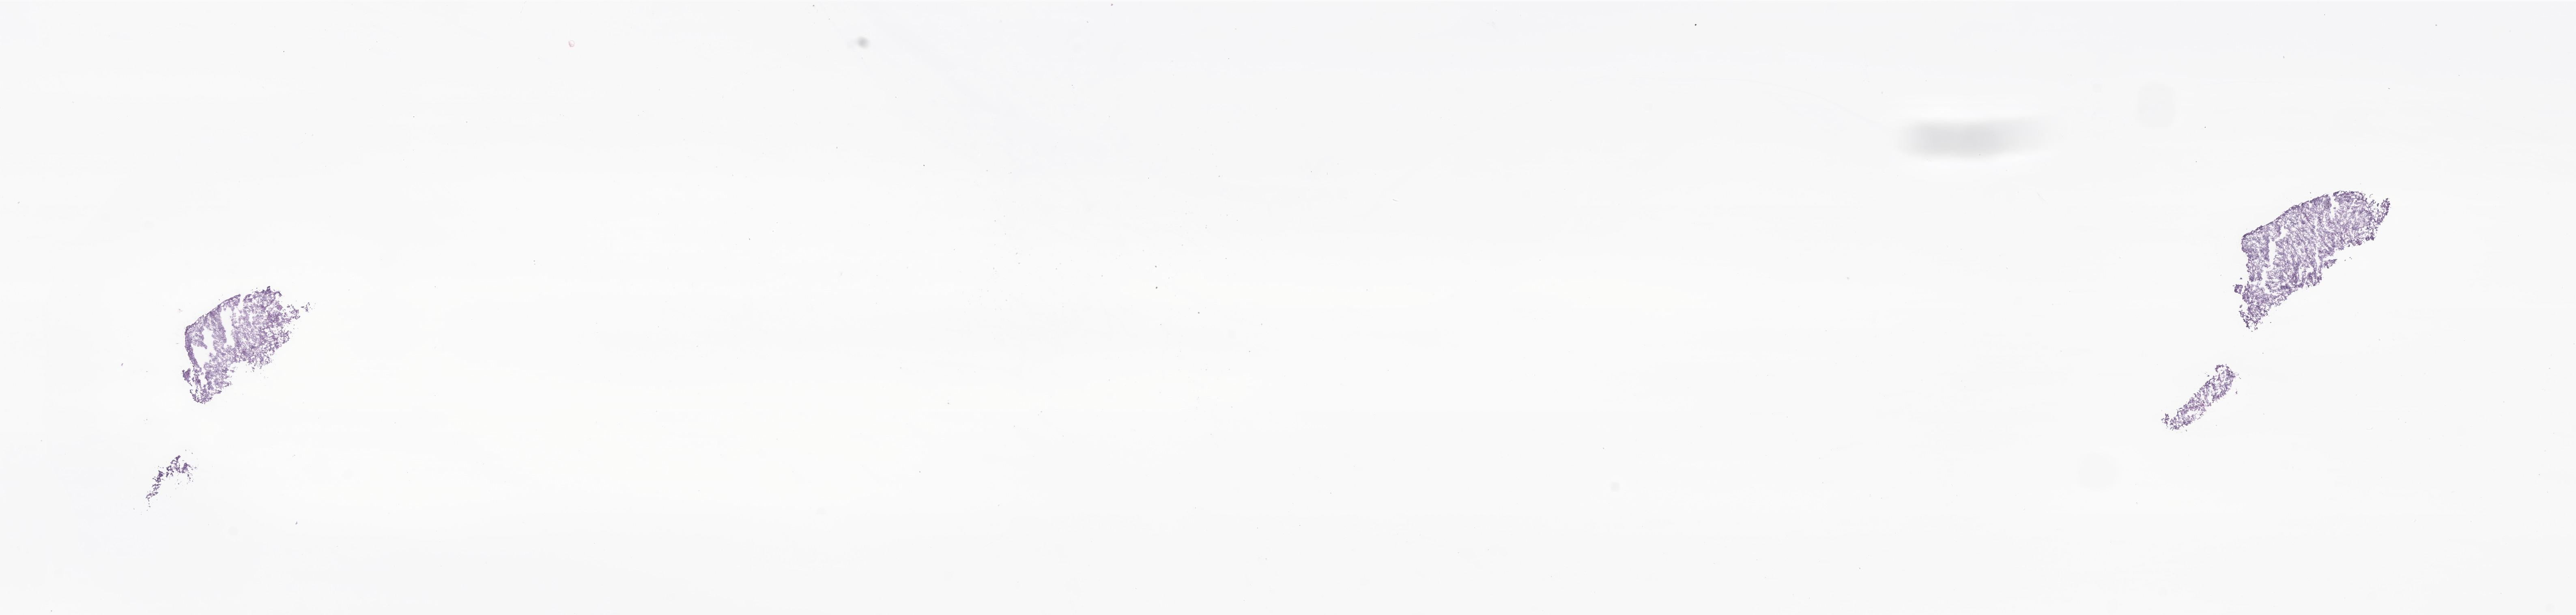
Haematoxylin and eosin whole-slide image of tumor tissue from the brain — a low-resolution overview of the entire scanned area, about 26.8 x 6.4 mm; cryosection (OCT / tissue freezing medium). Patient female; age 39 months (3 years 3 months).
Recorded diagnosis: Neoplasm, uncertain whether benign or malignant.